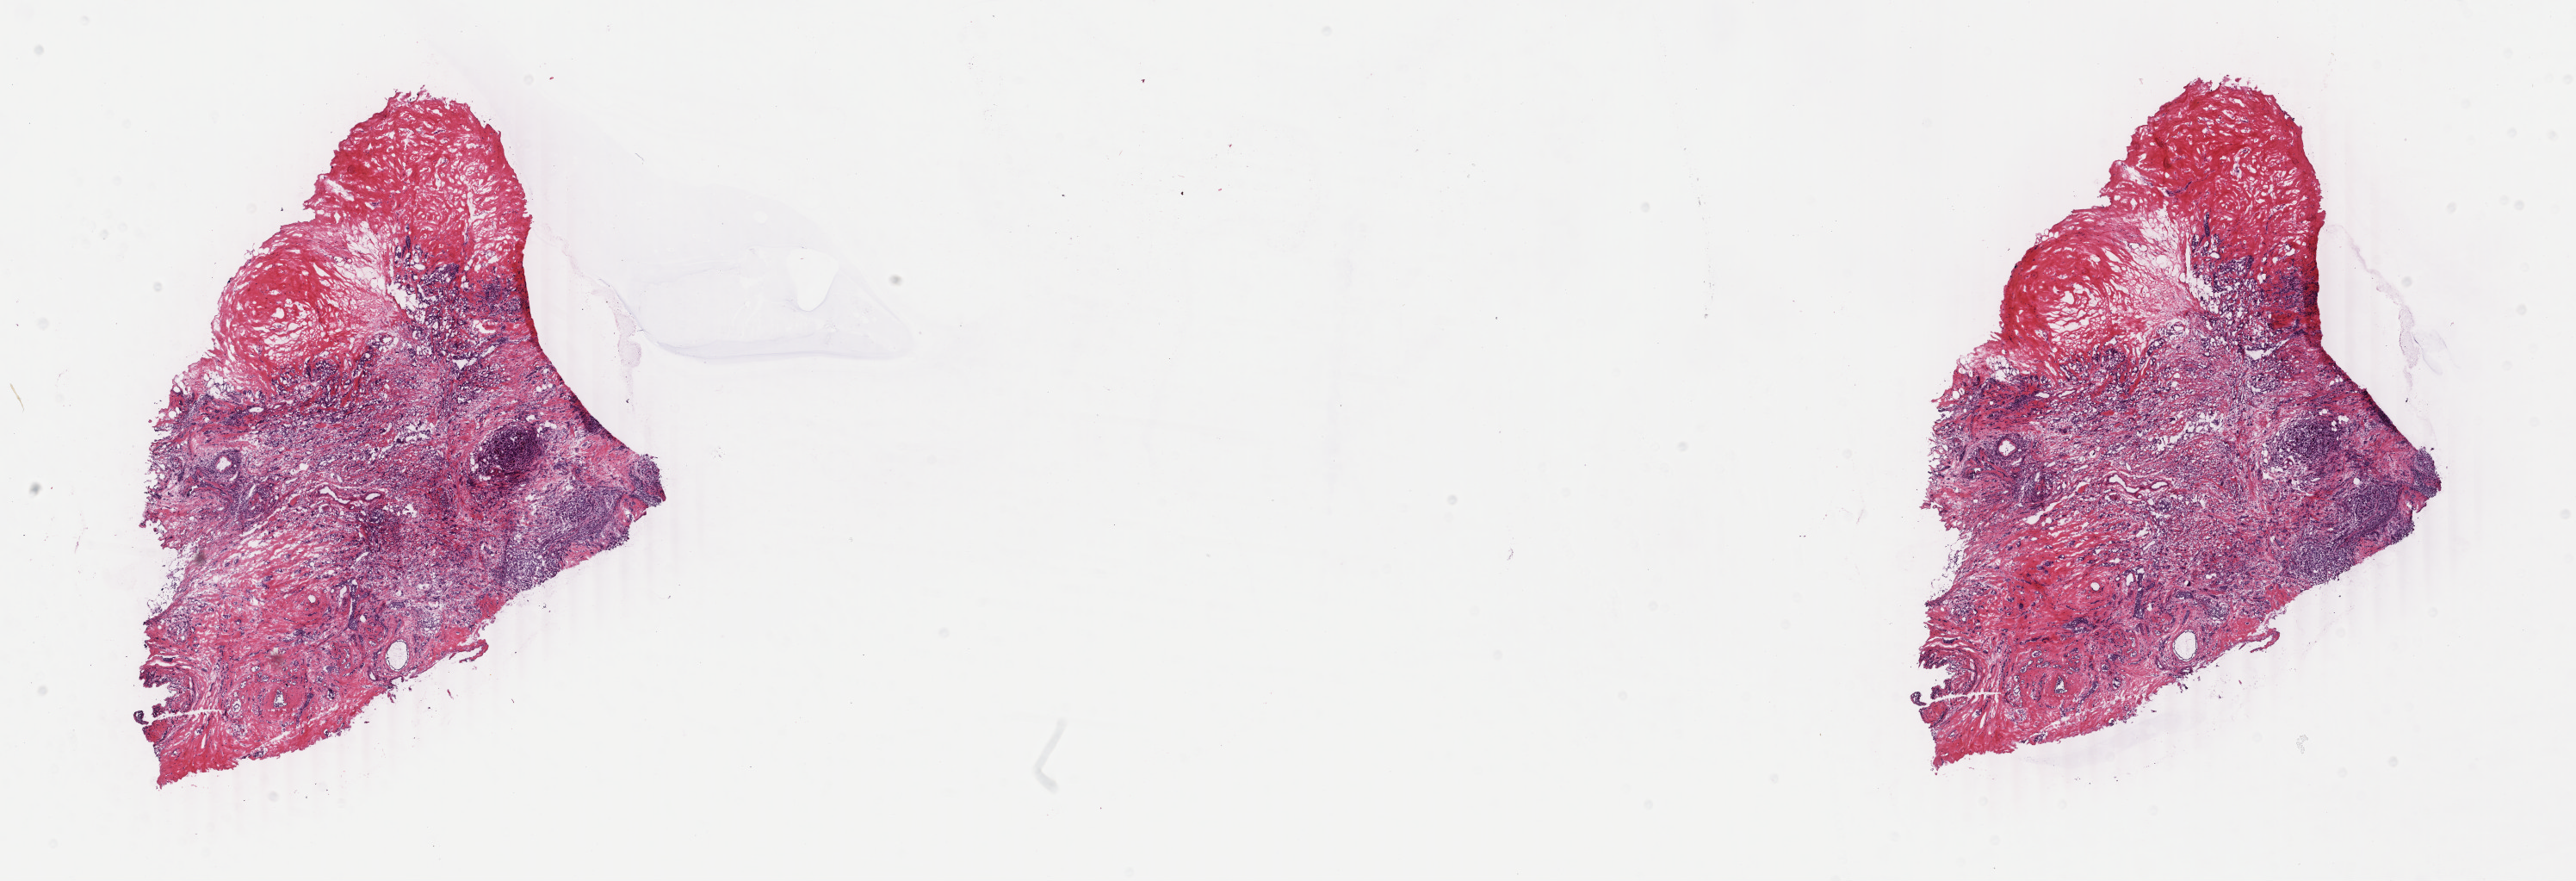
Whole-slide histology image, H&E-stained, a low-resolution overview of the entire scanned area, about 23.8 x 8.1 mm; frozen section from the bottom of the tissue portion; primary tumour sample from the breast. Female patient; age at initial diagnosis 42 years. Pathologist review of this section (percent, as recorded): tumour cells 70%, tumour nuclei 75%, normal cells 5%, stromal cells 25%, necrosis 0%. Infiltration values recorded for this section: lymphocyte infiltration 0%, monocyte infiltration 0%, neutrophil infiltration 0%.
AJCC pathologic stage: IIIA (4th edition). Laterality: right. Lymph nodes positive (case pathology): 5 of 10 examined. Pathologic diagnosis: Infiltrating duct and lobular carcinoma.